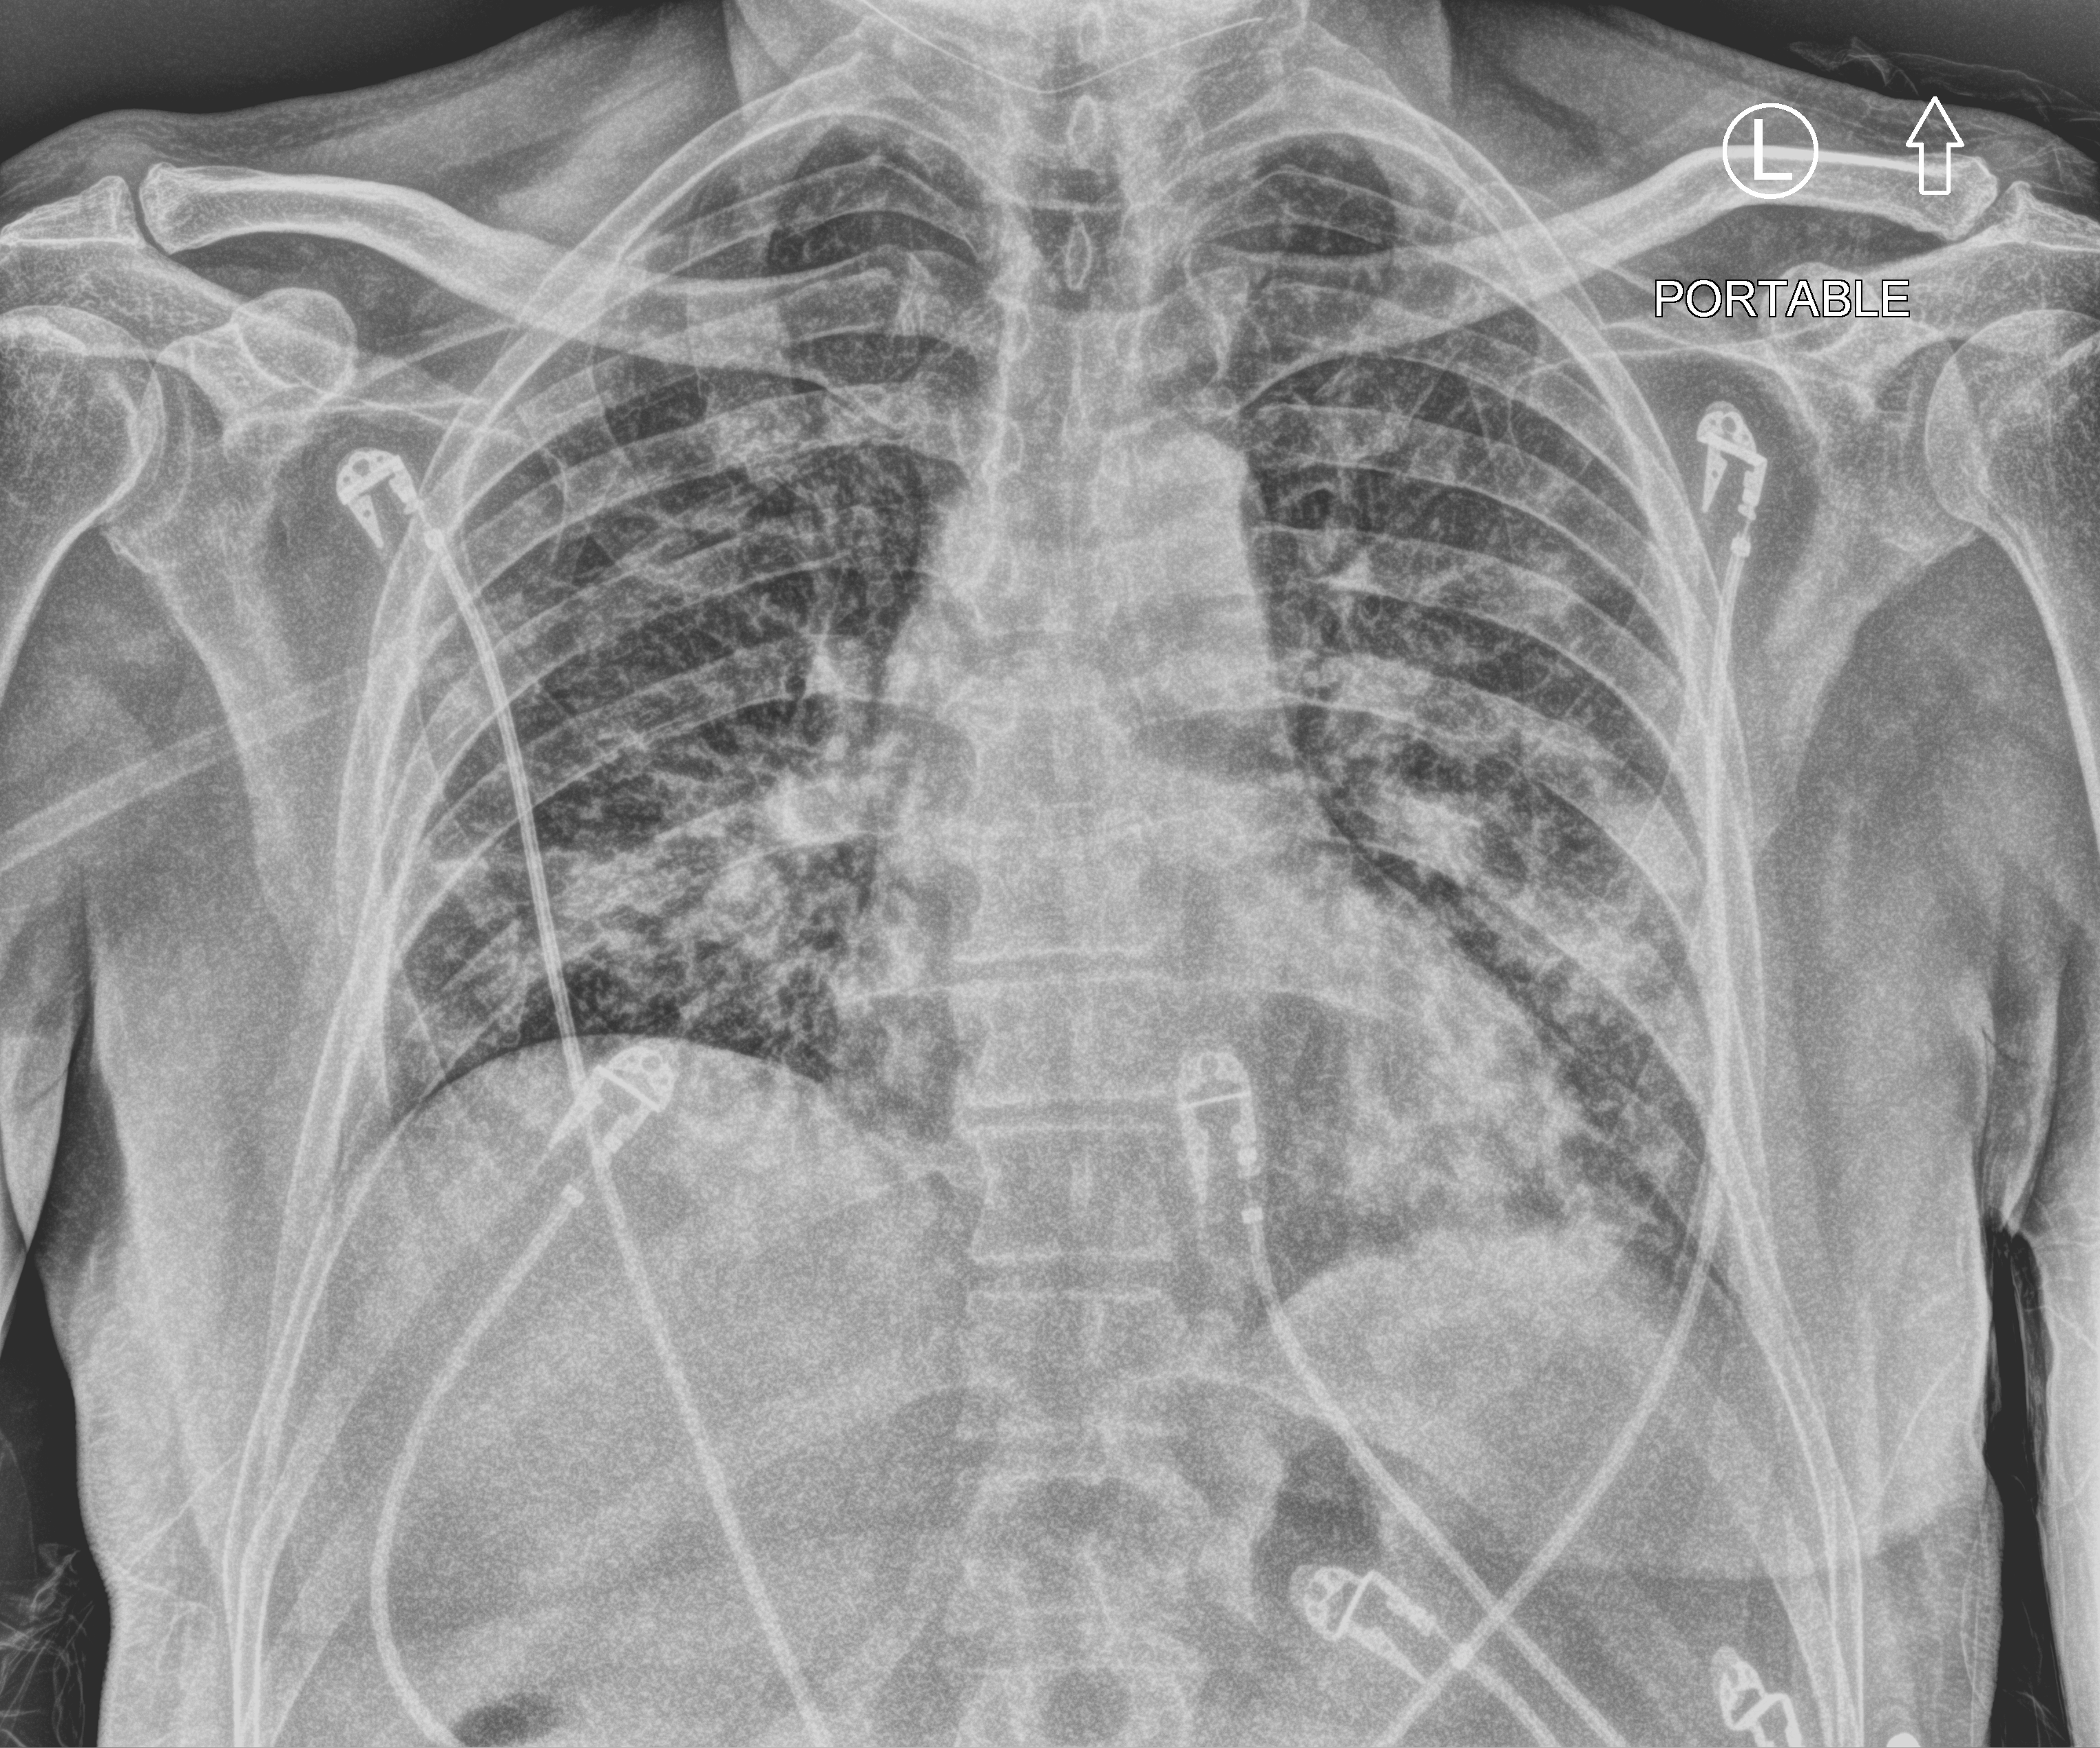
Bedside chest radiograph (computed radiography). Patient hospitalised with COVID-19; male, aged 60–74 years.
Hospital-stay facts (about this admission, not read from this image; timing relative to this image not recorded): mechanically ventilated during this hospital stay: no.